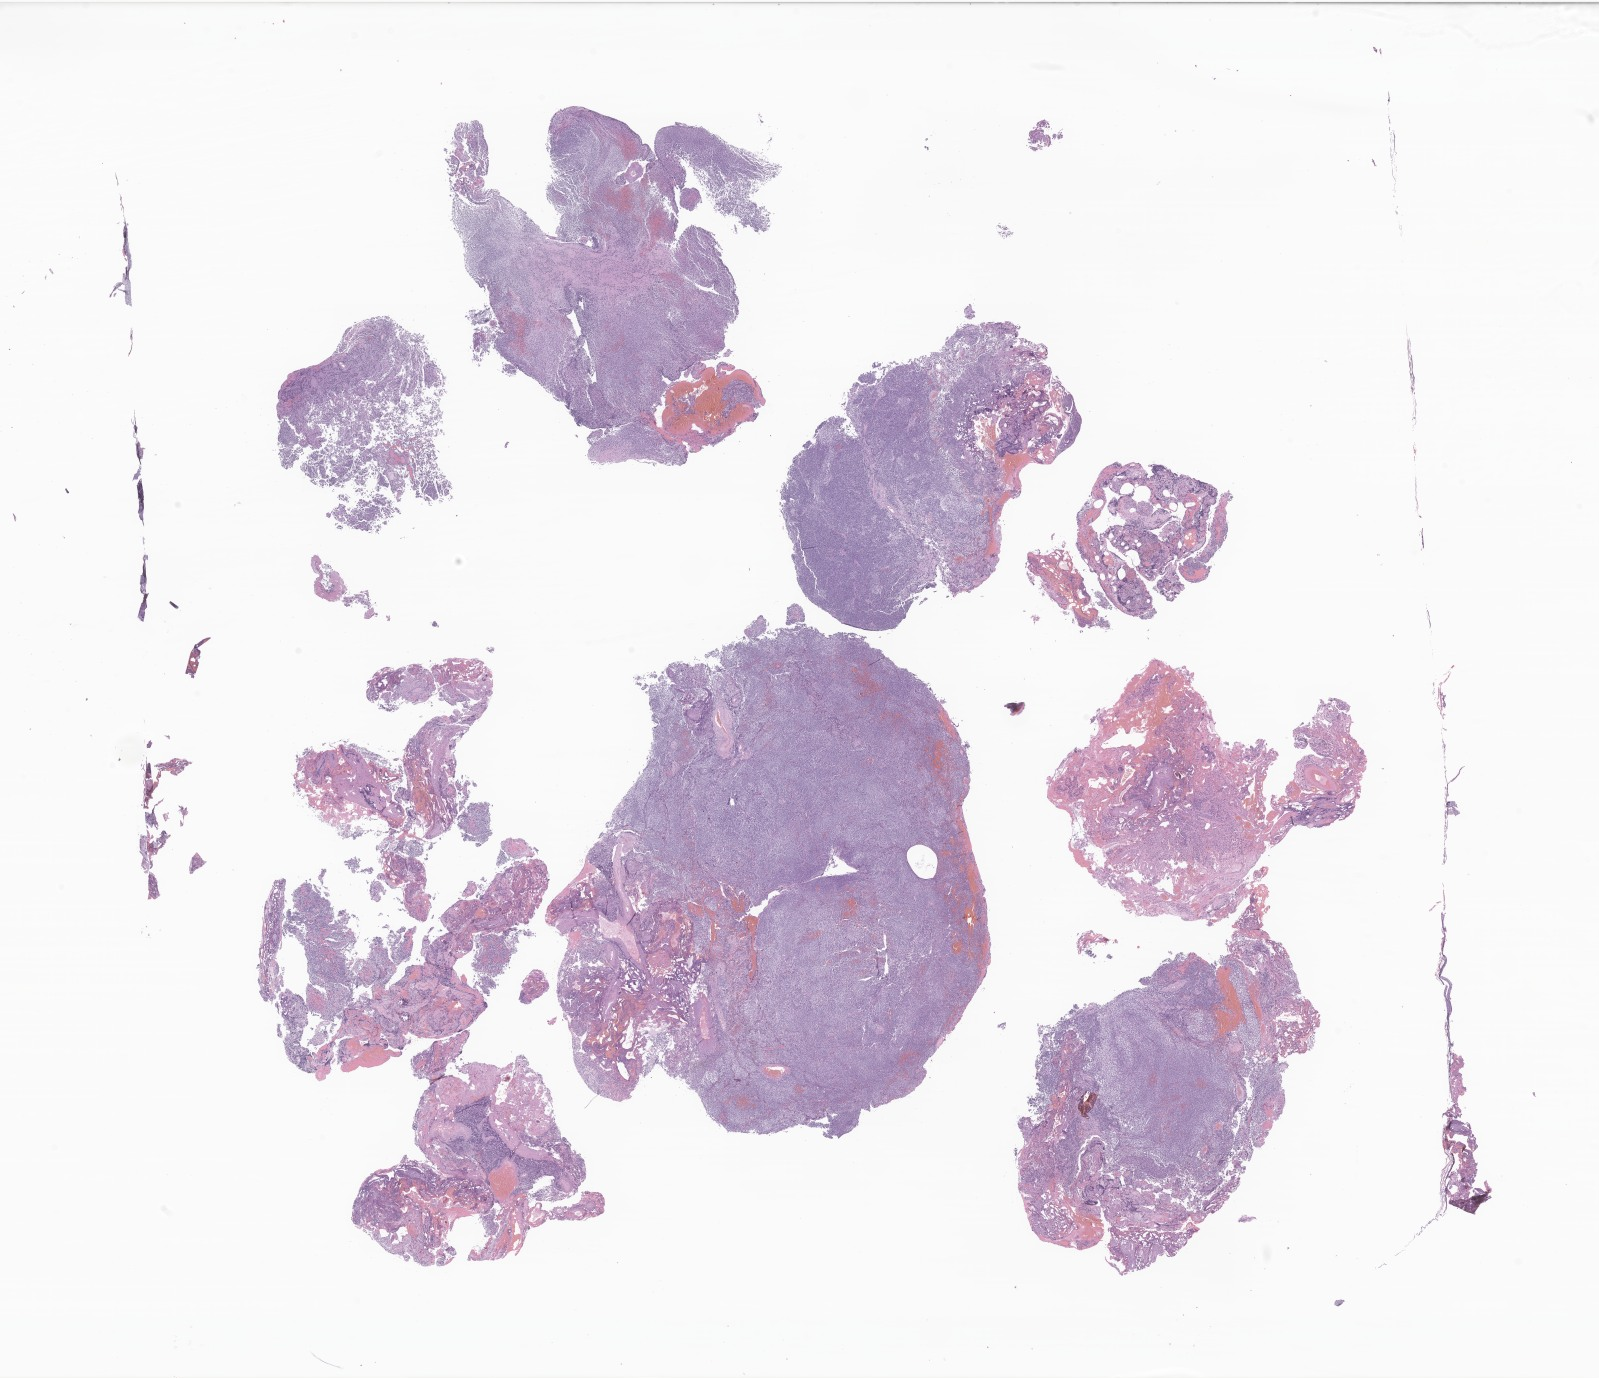
Whole-slide image, hematoxylin and eosin (H&E) stain of tumor tissue from the brain — shown as a low-resolution overview of the whole scanned area (about 27.0 x 23.2 mm), formalin-fixed, paraffin-embedded (FFPE) tissue. Male patient, age 74 months (6 years 2 months).
Diagnosis: Medulloblastoma, NOS.